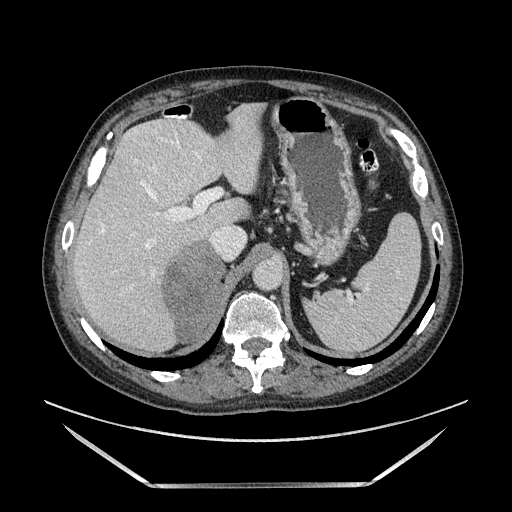
Contrast-enhanced abdominal CT, one axial slice. Position 103 of 185 along the scan axis. Soft-tissue window (W 400 / L 40 HU). 1.25 mm slice thickness. 512 × 512 image matrix, field of view 440 × 440 mm. Male patient. Case-level facts recorded for this patient, not image findings: diagnosis: adrenocortical carcinoma; tumour side: right adrenal; tumour size at pathology: 10.3 cm; Ki-67 index: 20 %; stage (as recorded): 3.
Annotated regions visible in this slice (semi-automatically segmented with operator editing):
- mass: bounding box <163,245,222,342> (left, top, right, bottom; pixels)